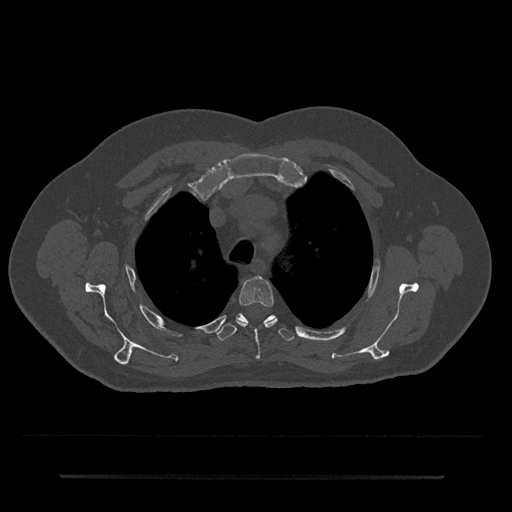
CT including the spine, one axial slice; slice 553 of 797 in the series (ordered by position); reconstruction kernel Br40s/3; bone window (W 1800 / L 400 HU); 0.5 mm slice thickness; 512 × 512 image matrix, field of view 437 × 437 mm. Male patient, age 69 years. Case-level facts recorded for this patient, not image findings: primary cancer: prostate.
Annotated regions visible in this slice (semi-automatic segmentation, software-assisted and operator-edited):
- T3 vertebra: bounding box [x1, y1, x2, y2] px = [236, 277, 278, 359]
- T4 vertebra: [216, 313, 294, 341]